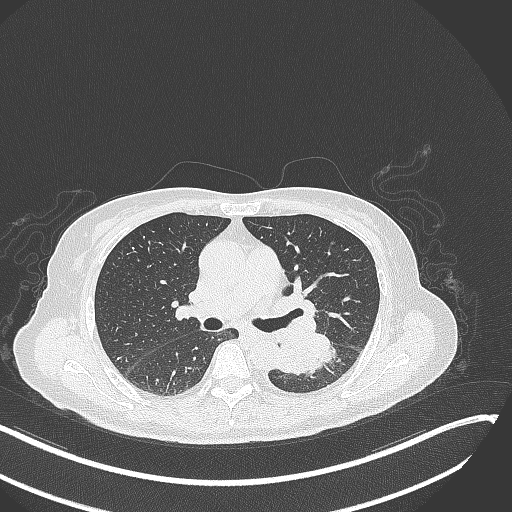
Chest CT, one axial slice; position 165 of 342 along the scan axis; 120 kVp; lung window (W 1500 / L -600 HU); 1 mm slice thickness; 512 × 512 image matrix, field of view 400 × 400 mm. Patient: female, 64 years. Case-level facts recorded for this patient, not image findings: clinical TNM (as recorded): T3 N1 M1; histopathological grade: G3.
Outlined on this slice (bounding box drawn by a radiologist):
- lung tumour (recorded histology: small cell carcinoma): bounding box <273,334,340,380> (left, top, right, bottom; pixels)